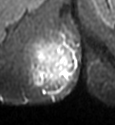
MRI of an extremity soft-tissue mass, one axial slice. Position 14 of 49 along the scan axis. STIR. MR volume resampled by the dataset authors to the PET/CT grid (not the native acquisition matrix). 3.27 mm slice thickness. 115 × 125 image matrix, field of view 112 × 122 mm. Female patient. Case-level facts recorded for this patient, not image findings: histological type: epithelioid sarcoma; grade: intermediate; site of the primary tumour: right buttock.
Outlined on this slice (expert contour drawn on MRI and transferred to this co-registered scan by the dataset authors):
- gross tumour volume including surrounding oedema: bounding box (x1, y1, x2, y2) in pixels: (24, 34, 80, 101)
- gross tumour volume (mass): (35, 43, 57, 63)